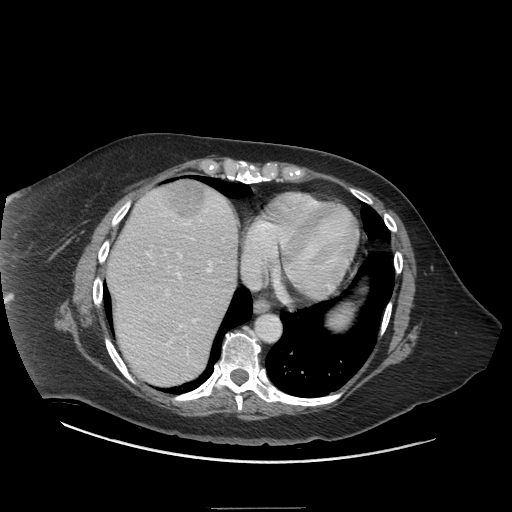
Contrast-enhanced abdominal CT (liver protocol), one axial slice; reconstruction kernel STANDARD; 140 kVp; soft-tissue window (W 400 / L 40 HU); 512 × 512 image matrix. From the clinical record (not read from this slice): diagnosis: hepatocellular carcinoma (patient treated with transarterial chemoembolisation; whether this scan precedes or follows treatment is not stated here); TNM stage (as recorded): Stage-II; Child-Pugh class: A; tumour nodularity: multinodular.
Annotated regions visible in this slice (semi-automatic segmentation, software-assisted and operator-edited):
- abdominal aorta: bounding box (x1, y1, x2, y2) in pixels: (256, 315, 279, 341)
- liver parenchyma outside the tumour (the mass and vessels are separate outlines, so this box may not span the whole liver): (106, 180, 236, 386)
- mass: (167, 181, 207, 215)
- liver vessels: (121, 198, 226, 366)